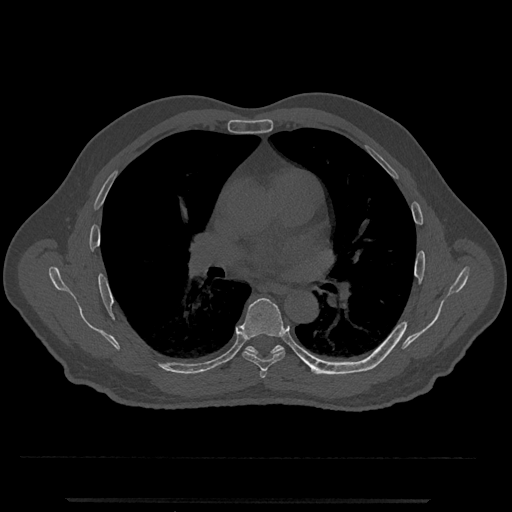
CT including the spine, one axial slice. Position 723 of 797 along the scan axis. Reconstruction kernel Br40s/3. 120 kVp. Bone window (W 1800 / L 400 HU). 0.5 mm slice thickness. 512 × 512 image matrix. Patient: male, 63 years. From the clinical record (not read from this slice): primary cancer: prostate.
Annotated regions visible in this slice (semi-automatic segmentation, software-assisted and operator-edited):
- T5 vertebra: box from (x=260, y=370) to (x=267, y=378) px
- T6 vertebra: (x=239, y=298)–(x=285, y=372)
- T7 vertebra: (x=245, y=345)–(x=330, y=375)